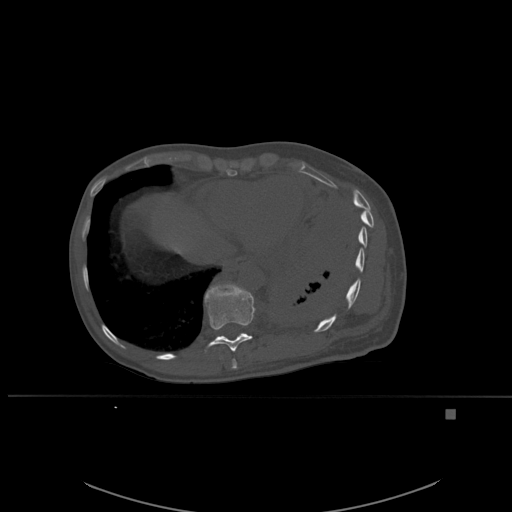
CT including the spine, one axial slice. Position 316 of 537 along the scan axis. Bone window (W 1800 / L 400 HU). 1.5 mm slice thickness. 512 × 512 image matrix, field of view 440 × 440 mm. Female patient, age 45 years. From the clinical record (not read from this slice): primary cancer: lung.
Outlined on this slice (semi-automatically segmented with operator editing):
- T10 vertebra: box from (x=204, y=284) to (x=256, y=352) px
- T11 vertebra: (x=216, y=282)–(x=234, y=340)
- T9 vertebra: (x=232, y=359)–(x=237, y=369)